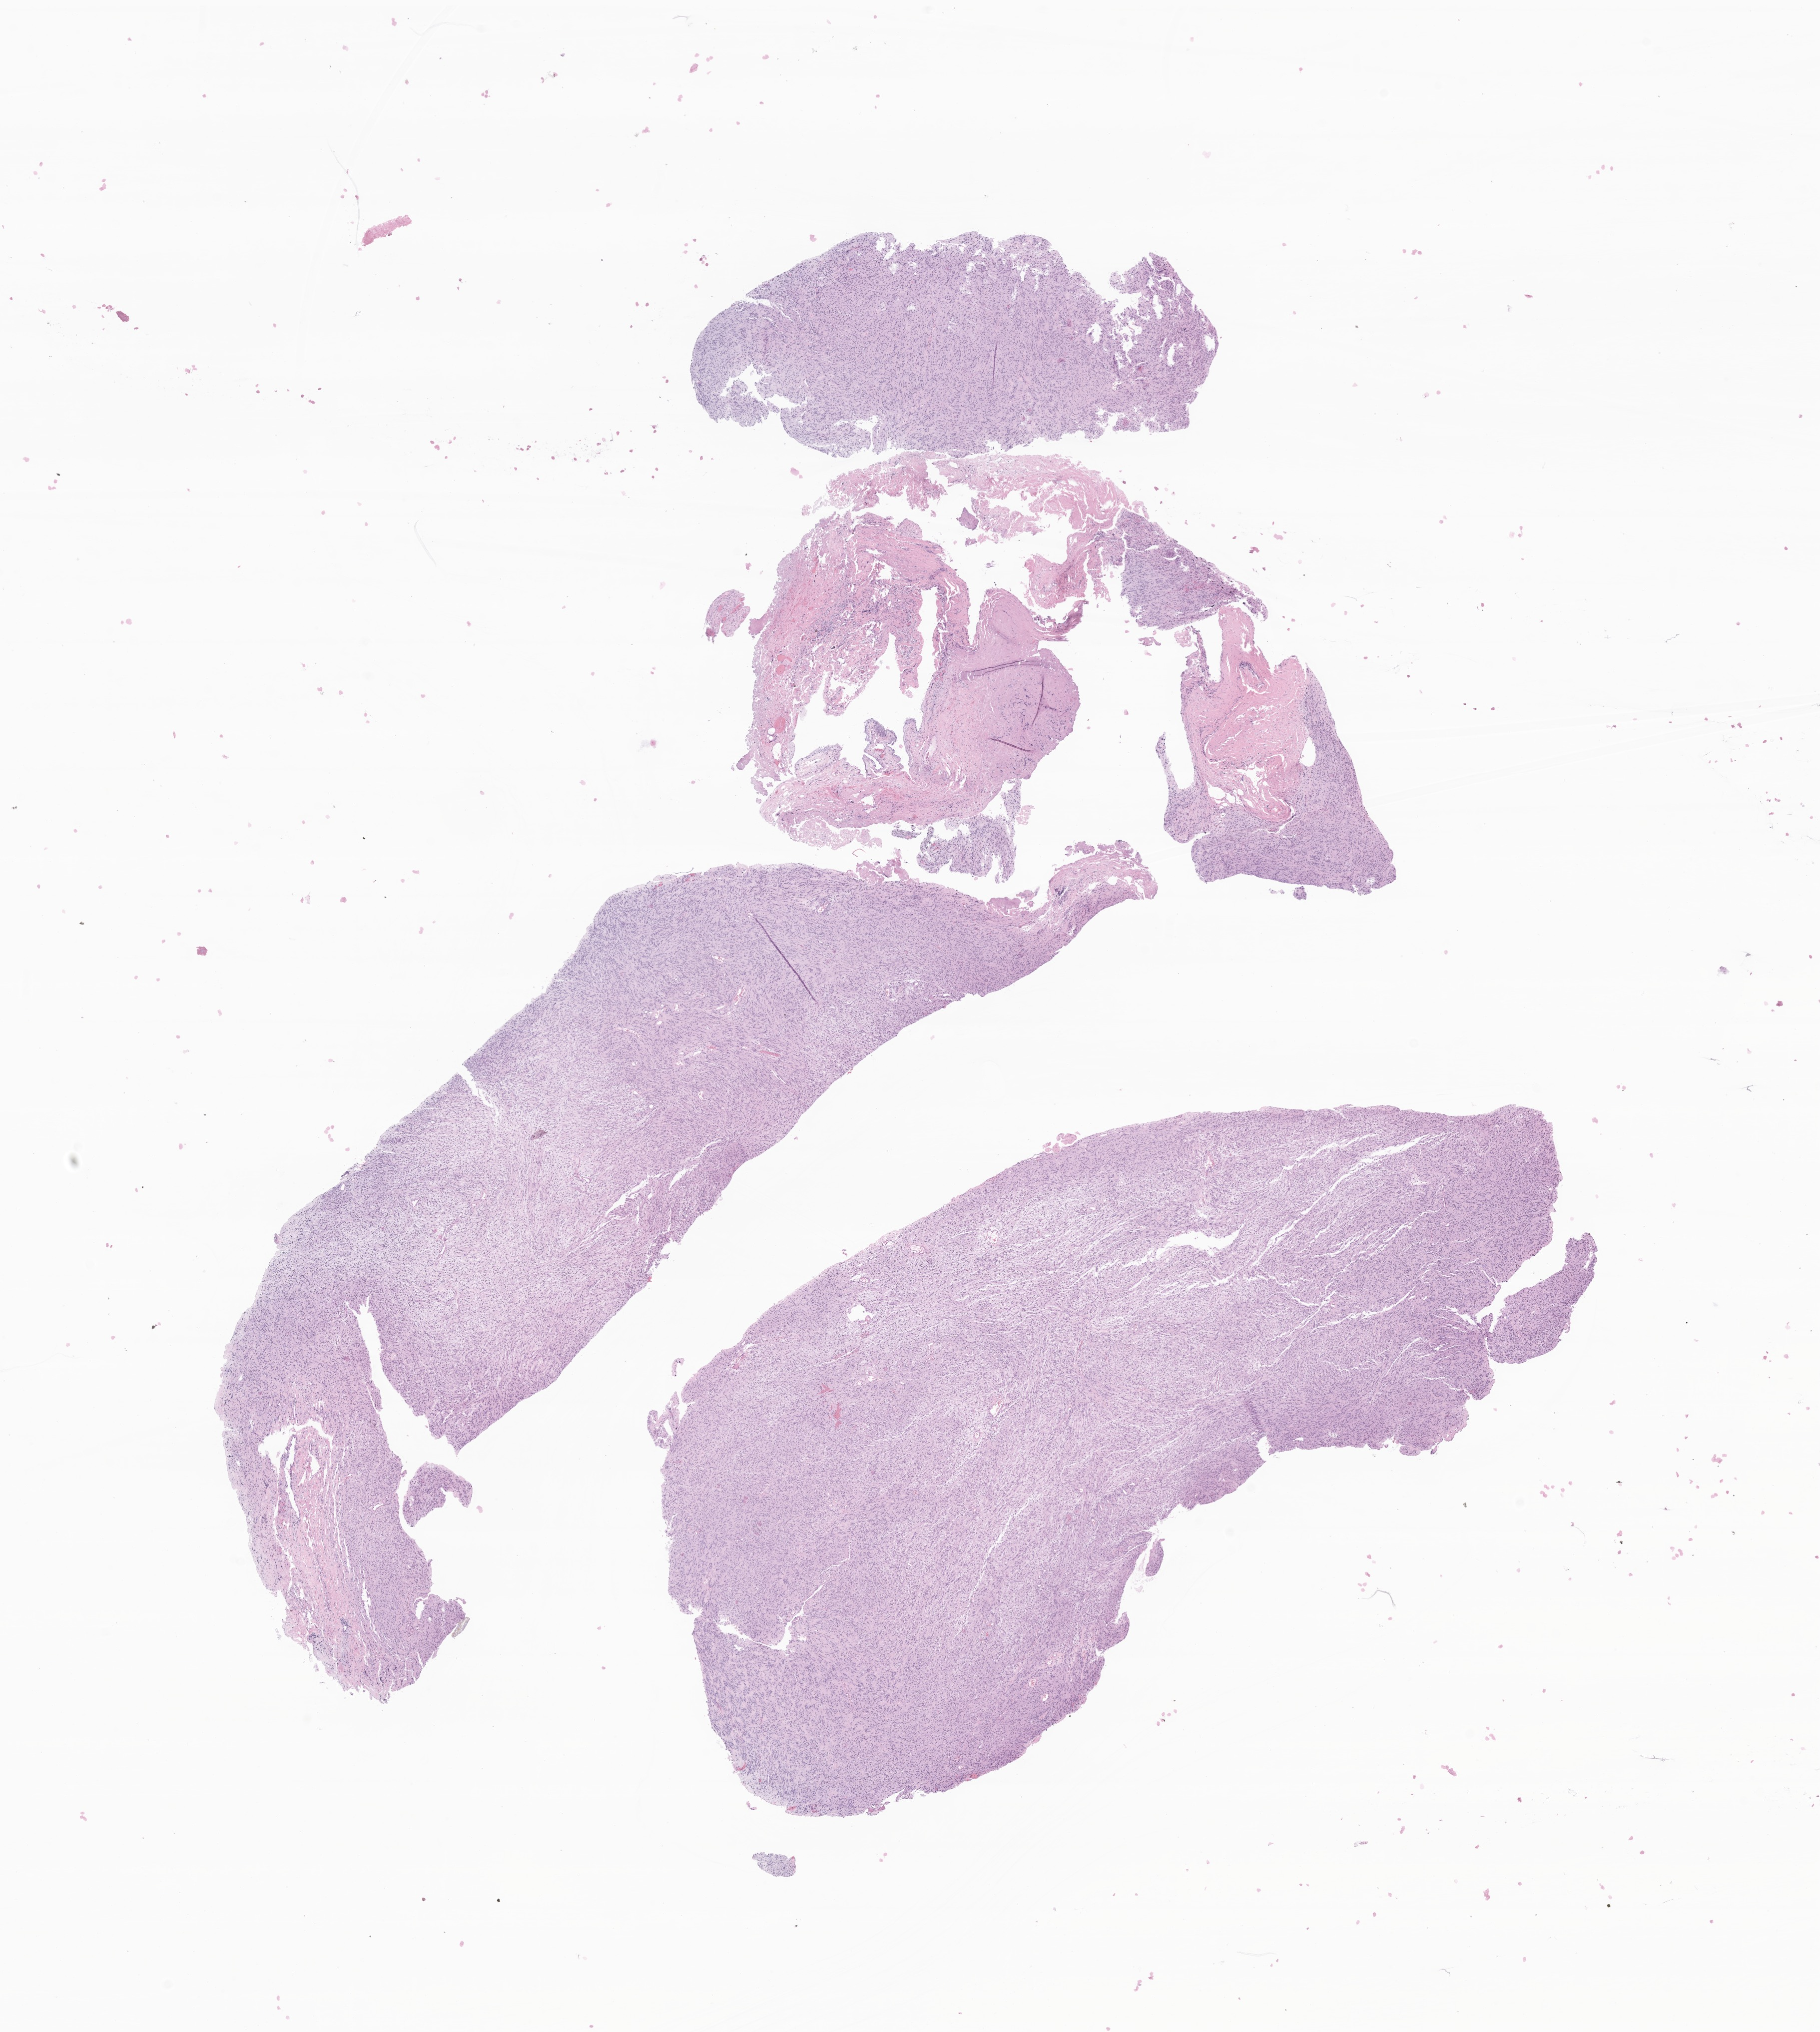
Digitized hematoxylin and eosin (H&E)-stained section of tumor tissue from the spinal cord, a low-resolution overview of the entire scanned area, about 15.4 x 17.1 mm, FFPE section. Patient: female, age 217 months (18 years 1 month).
Diagnosis (ICD-O-3 morphology term): Schwannoma, NOS.